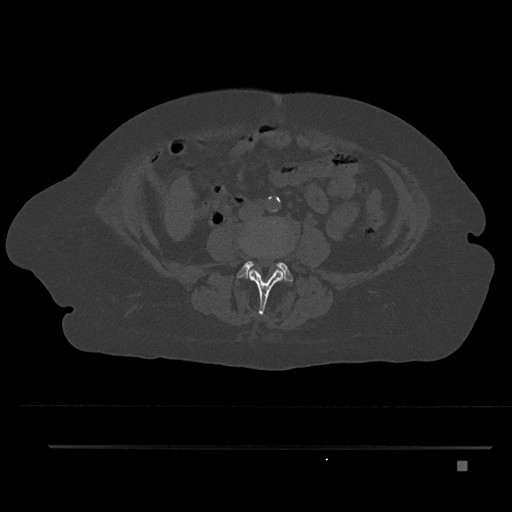
CT including the spine, one axial slice; slice 107 of 797 in the series (ordered by position); reconstruction kernel Br40s/3; bone window (W 1800 / L 400 HU); 512 × 512 image matrix, field of view 437 × 437 mm. Patient: female, 76 years. From the clinical record (not read from this slice): primary cancer: lung; vertebrae with lytic lesions (as recorded): T11, L3.
Annotated regions visible in this slice (semi-automatically segmented with operator editing):
- L3 vertebra: bounding box (x1, y1, x2, y2) in pixels: (249, 269, 285, 314)
- L4 vertebra: (237, 224, 293, 281)